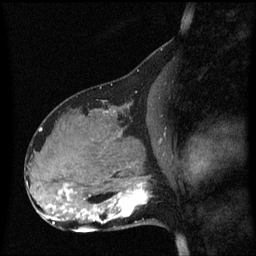
Breast MRI (dynamic contrast-enhanced), one sagittal slice; dynamic contrast-enhanced series, image 2 of 3 at this slice position (ordered by acquisition); 1.5 T; TE 4.2 ms, TR 8.4 ms; 2.1 mm slice thickness; 256 × 256 image matrix, field of view 210 × 210 mm. Patient: female, 31 years. Case-level facts recorded for this patient, not image findings: setting: breast cancer imaged before/during neoadjuvant chemotherapy; receptor status: HR-positive, HER2-negative.
Structures marked on this image (semi-automatically segmented with operator editing):
- analysis volume of interest (the breast-tissue region the enhancement analysis was run in; not a lesion): box from (x=98, y=175) to (x=155, y=228) px
- tumour enhancement mask (voxels above the 70 % enhancement threshold inside the analysis volume of interest): (x=98, y=183)–(x=149, y=225)